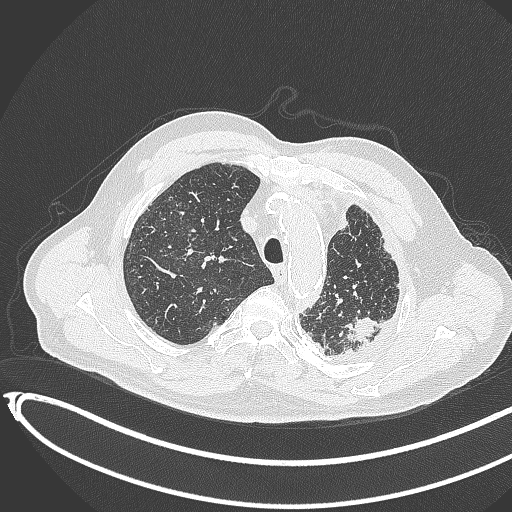
Chest CT, one axial slice; position 340 of 451 along the scan axis; lung window (W 1500 / L -600 HU); 1 mm slice thickness; 512 × 512 image matrix. Male patient, age 78 years. From the clinical record (not read from this slice): clinical TNM (as recorded): T1c N0 M1.
Outlined on this slice (rectangle marked by the reading radiologist):
- lung tumour (recorded histology: adenocarcinoma): bounding box (x1, y1, x2, y2) in pixels: (342, 318, 380, 343)